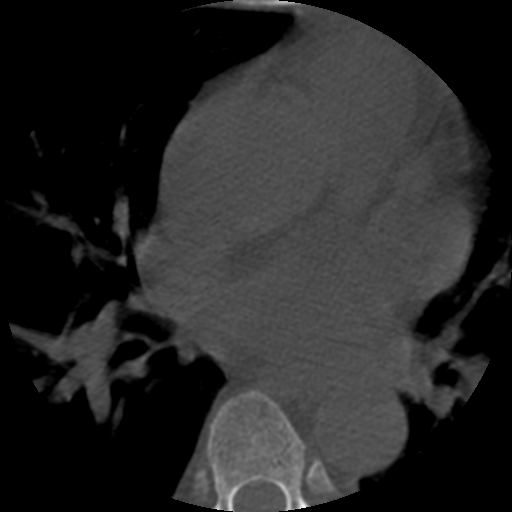
CT including the spine, one axial slice. Slice 357 of 508 in the series (ordered by position). Reconstruction kernel STANDARD. 120 kVp. Bone window (W 1800 / L 400 HU). 1.25 mm slice thickness. 512 × 512 image matrix, field of view 160 × 160 mm. Patient age 57 years. From the clinical record (not read from this slice): primary cancer: prostate.
Outlined on this slice (semi-automatically segmented with operator editing):
- T6 vertebra: box from (x=207, y=391) to (x=307, y=512) px